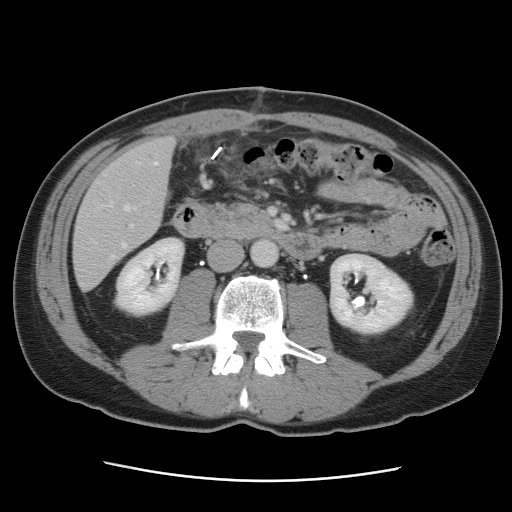
Contrast-enhanced abdominal CT, one axial slice; intravenous contrast given; soft-tissue window (W 400 / L 40 HU); 5 mm slice thickness; 512 × 512 image matrix, field of view 366 × 366 mm. Male patient, age 59 years. From the clinical record (not read from this slice): diagnosis: colorectal cancer liver metastases, imaged before liver resection; multiple liver metastases: yes; largest metastasis: 0.6 cm; disease in both lobes: yes.
Annotated regions visible in this slice (outlined manually by an expert reader):
- hepatic veins: bounding box [x1, y1, x2, y2] px = [93, 162, 157, 260]
- liver: [74, 139, 174, 289]
- planned liver remnant (the part of the liver to remain after resection): [74, 139, 175, 247]
- portal vein (with intrahepatic branches): [130, 224, 134, 228]